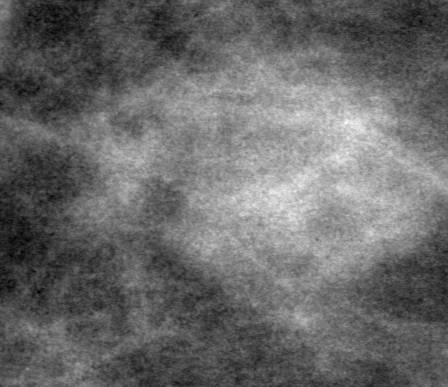
Cropped region of a digitized screen-film mammogram centred on a radiologist-marked abnormality, left breast, MLO view, BI-RADS breast density category 1 (scale 1–4).
Finding: mass, shape irregular, margins obscured; BI-RADS assessment category 0 (incomplete: needs additional imaging); subtlety rating 4 on a 1 (subtle) to 5 (obvious) scale; pathology result (as recorded, not read from the image): benign.